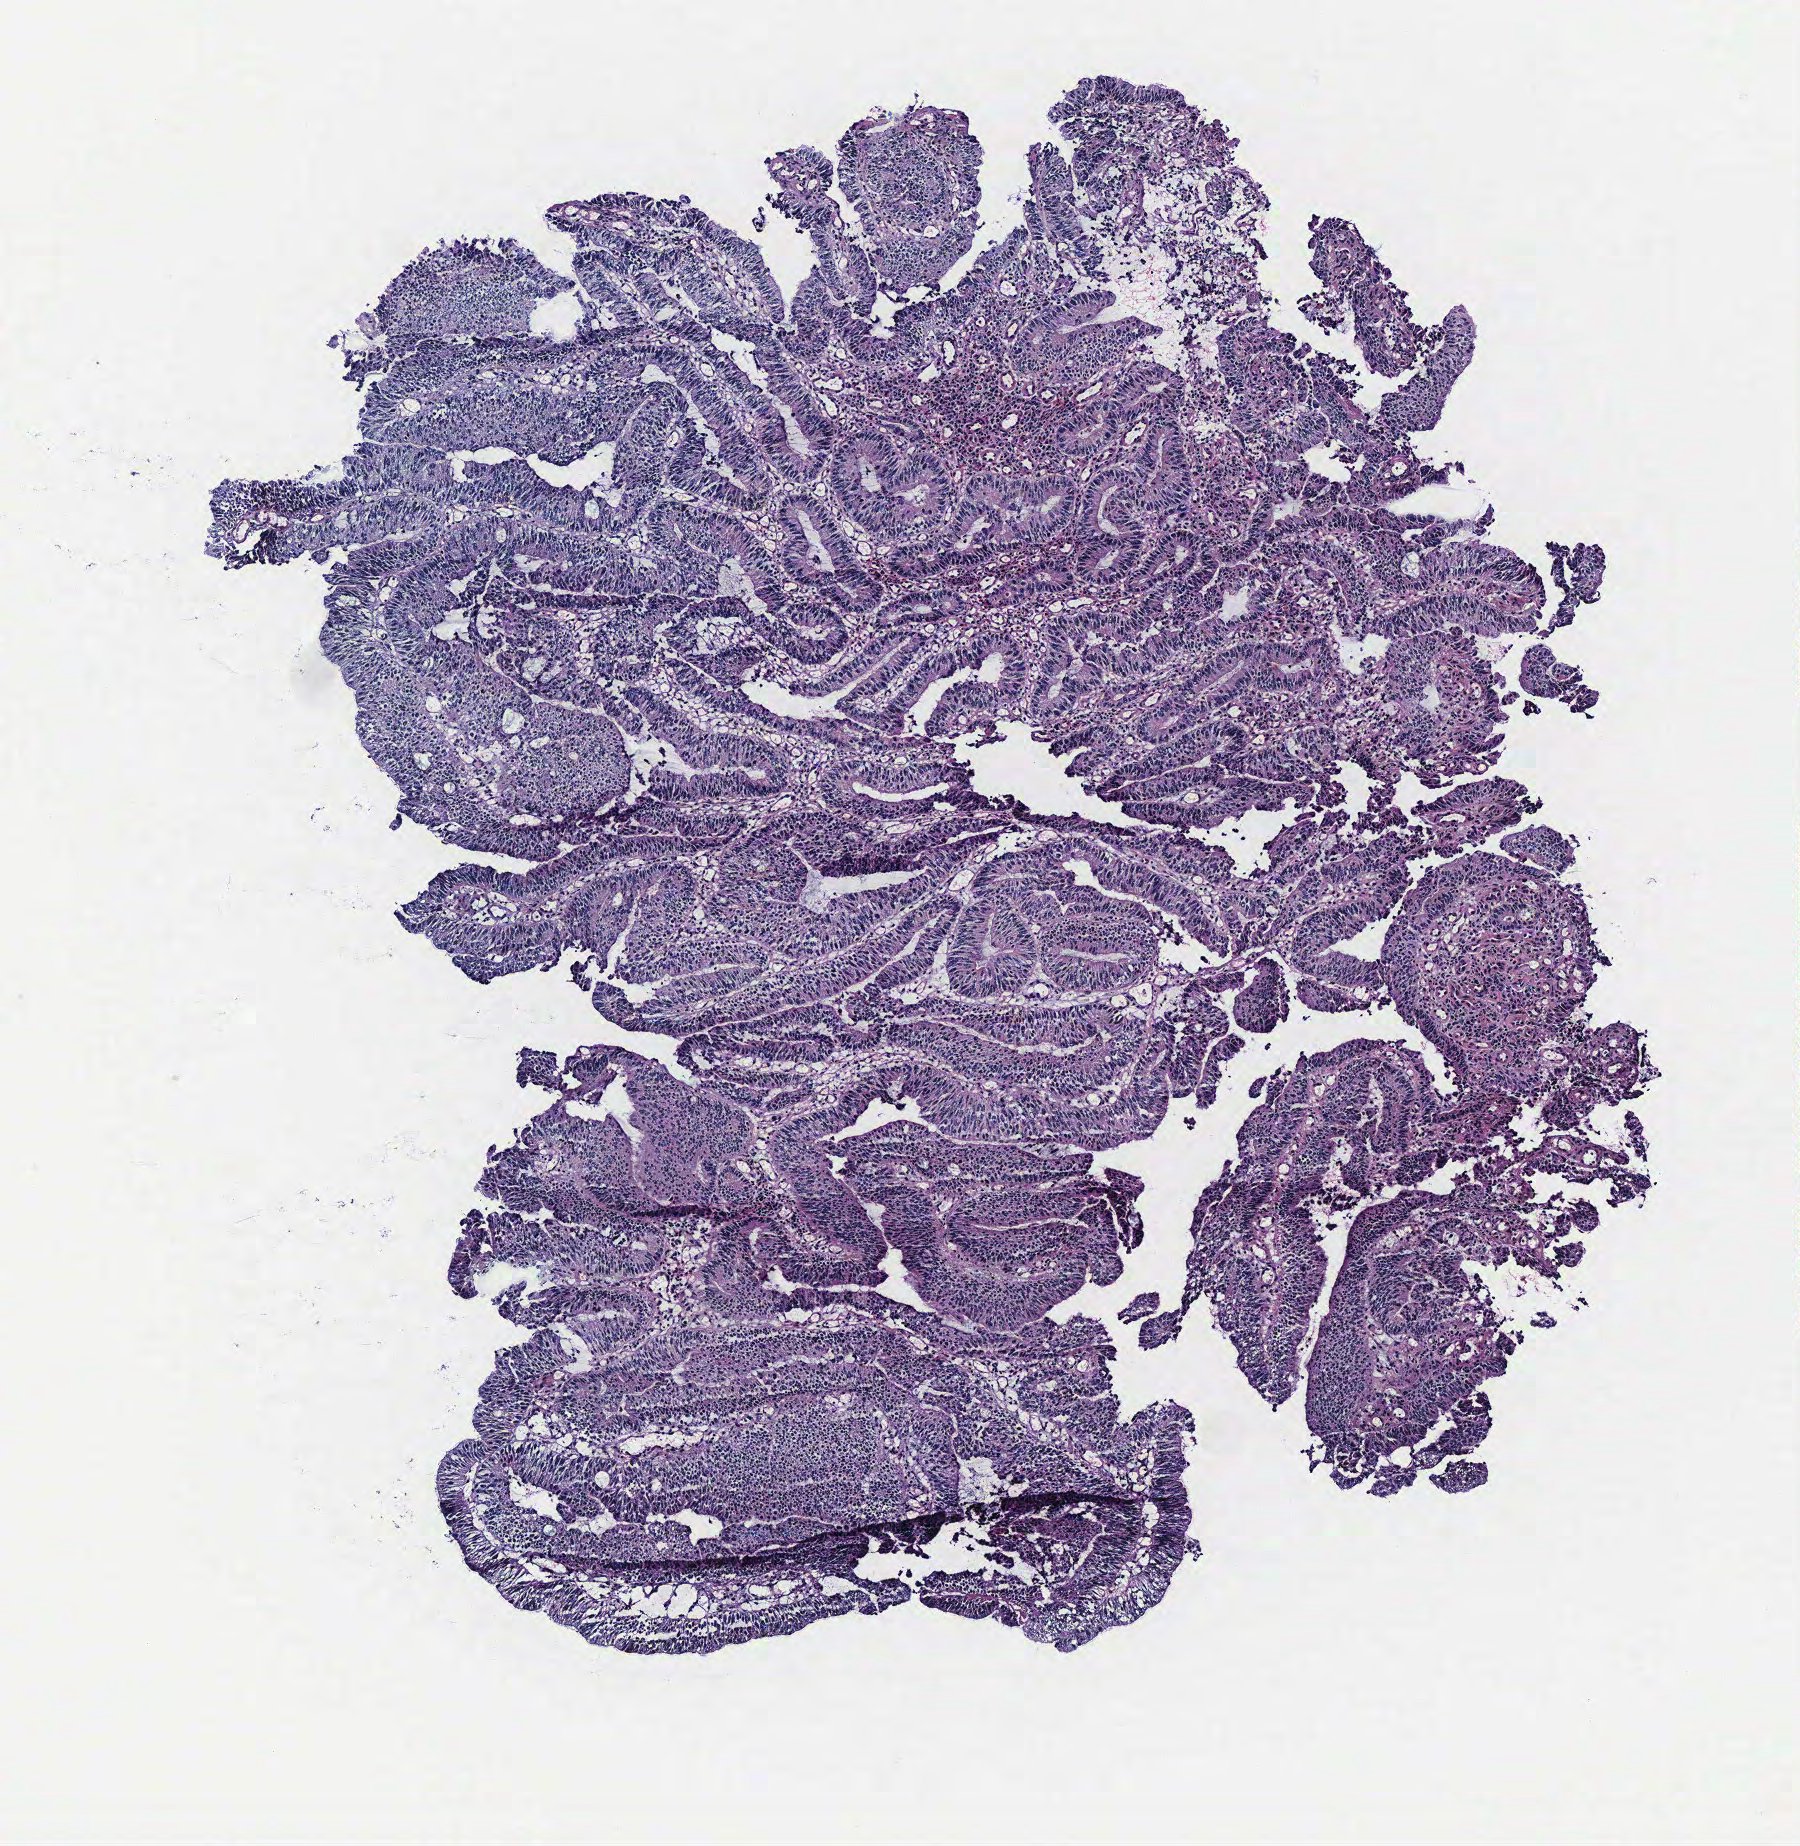
Whole-slide histology image, H&E-stained — shown as a low-resolution overview of the whole scanned area (about 3.6 x 3.7 mm, slide scanned at 40x); colon, tissue type not recorded.
• patient diagnosis (cohort enrolment): colon cancer (colon)